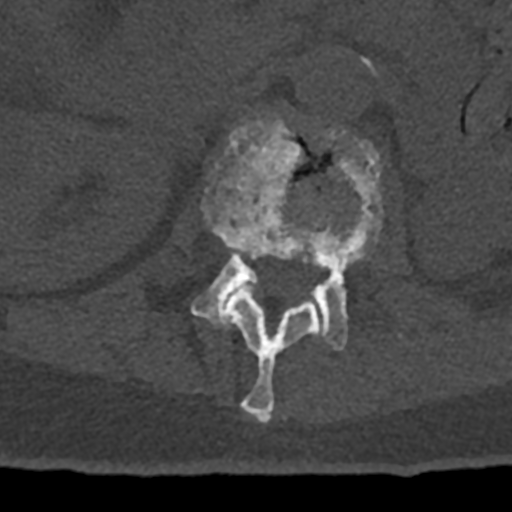
CT including the spine, one axial slice; position 407 of 797 along the scan axis; 120 kVp; bone window (W 1800 / L 400 HU); 0.5 mm slice thickness; 512 × 512 image matrix. Male patient, age 74 years. From the clinical record (not read from this slice): primary cancer: renal.
Annotated regions visible in this slice (semi-automatically segmented with operator editing):
- L1 vertebra: bounding box (x1, y1, x2, y2) in pixels: (202, 118, 339, 423)
- L2 vertebra: (192, 130, 383, 351)